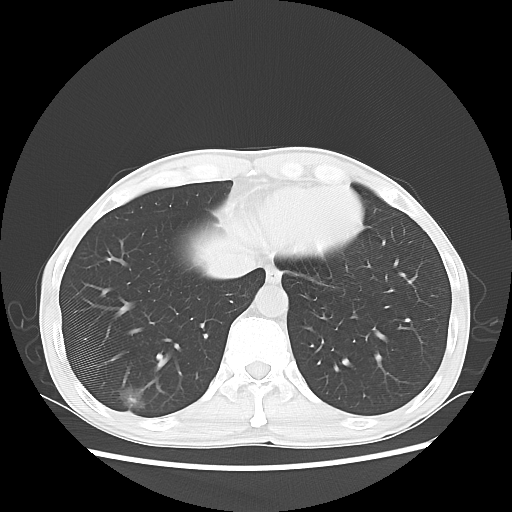
Chest CT, one axial slice; slice 18 of 68 in the series (ordered by position); 100 kVp; lung window (W 1500 / L -600 HU); 512 × 512 image matrix, field of view 360 × 360 mm. Male patient, age 60 years. From the clinical record (not read from this slice): clinical TNM (as recorded): T1c N0 M0; histopathological grade: G2.
Annotated regions visible in this slice (rectangle marked by the reading radiologist):
- lung tumour (recorded histology: adenocarcinoma): bounding box (x1, y1, x2, y2) in pixels: (121, 384, 151, 422)